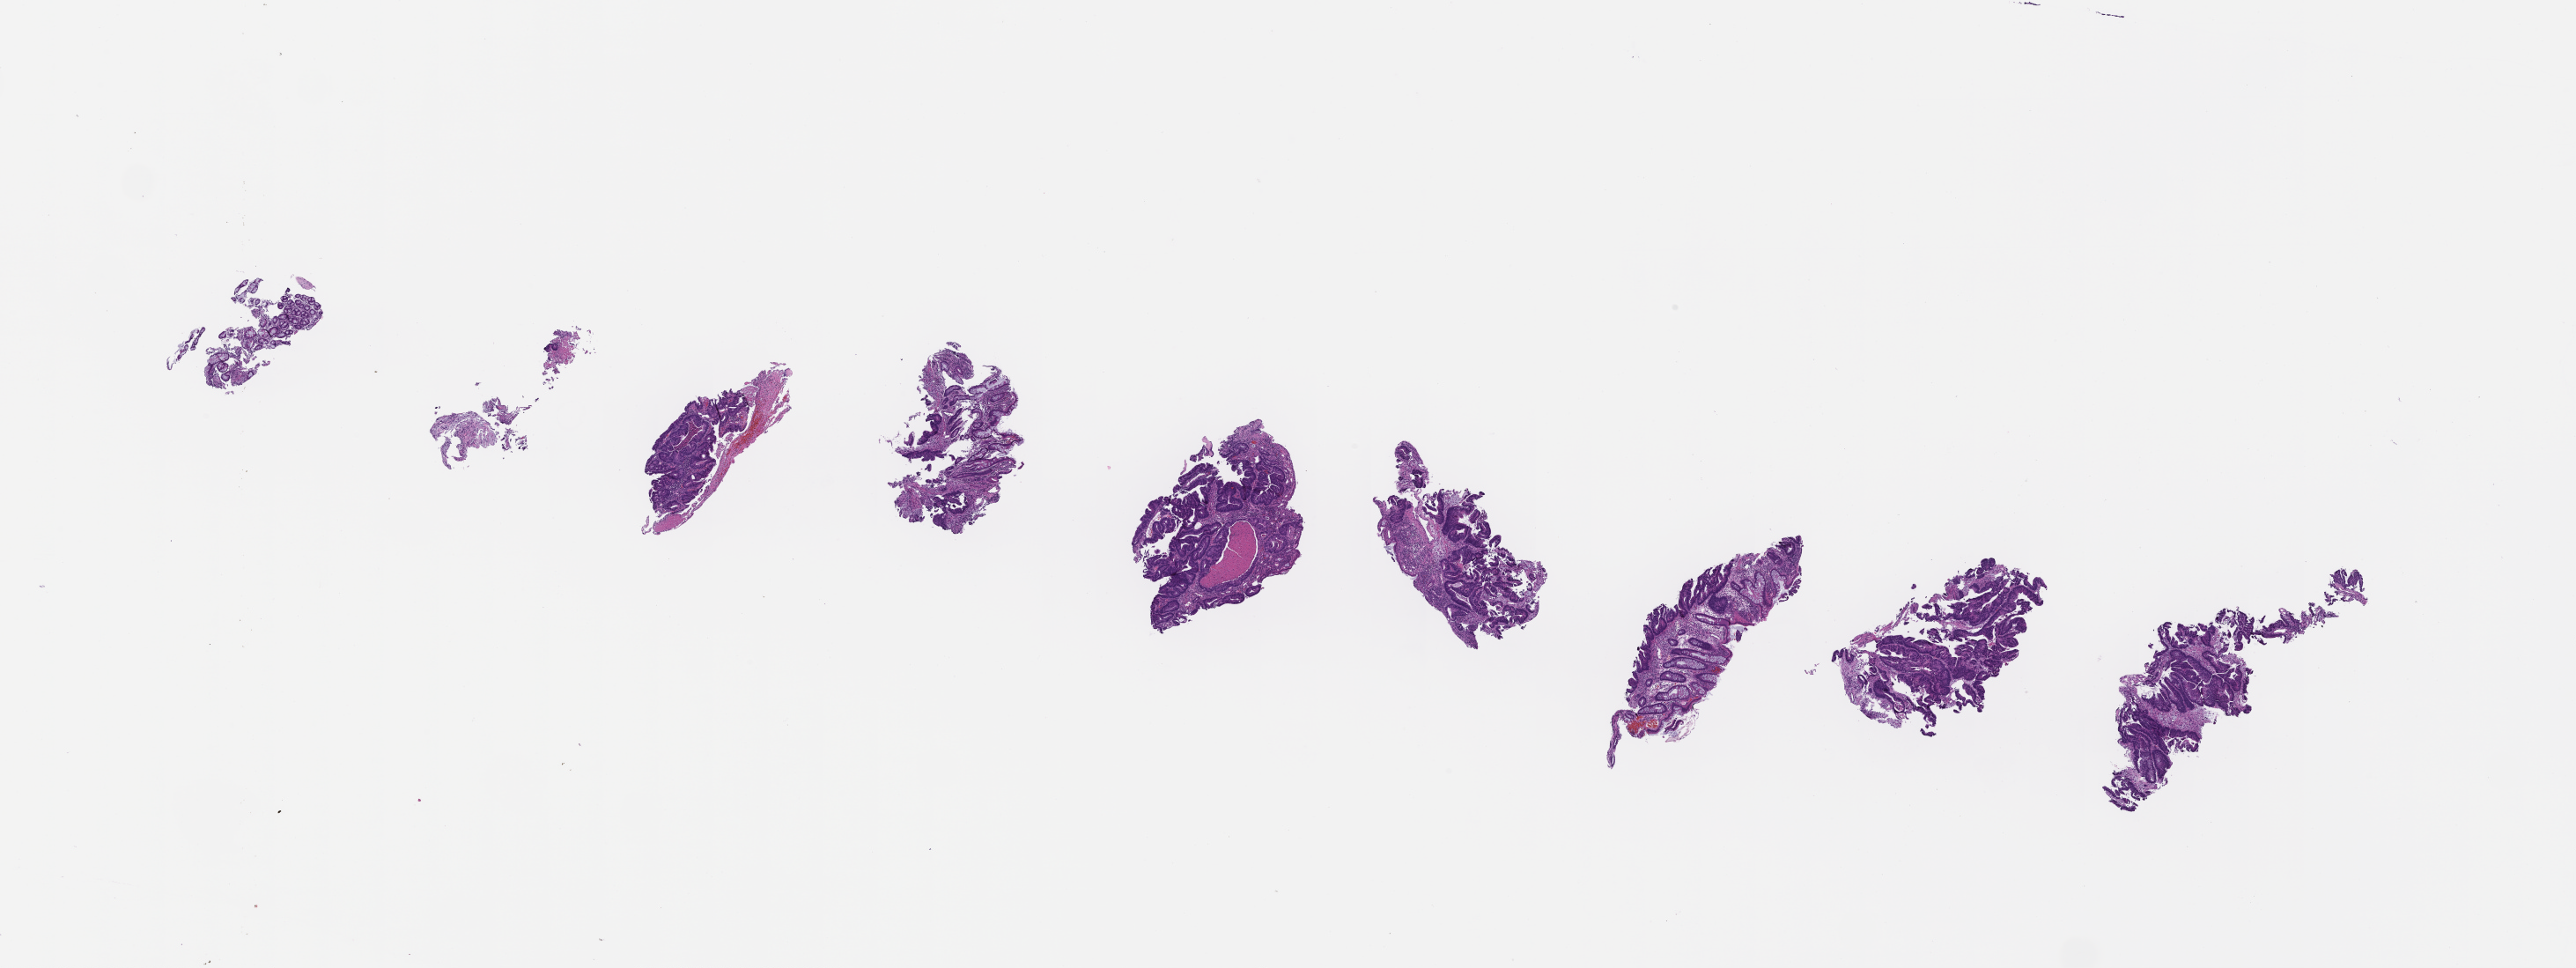
Haematoxylin and eosin whole-slide image — a low-resolution overview of the entire scanned area, about 23.6 x 8.9 mm, formalin-fixed paraffin-embedded section, tissue site: colon, specimen time point: archival tissue. Patient sex: male.
This section: primary tumor. Diagnosis: Colorectal Carcinoma.